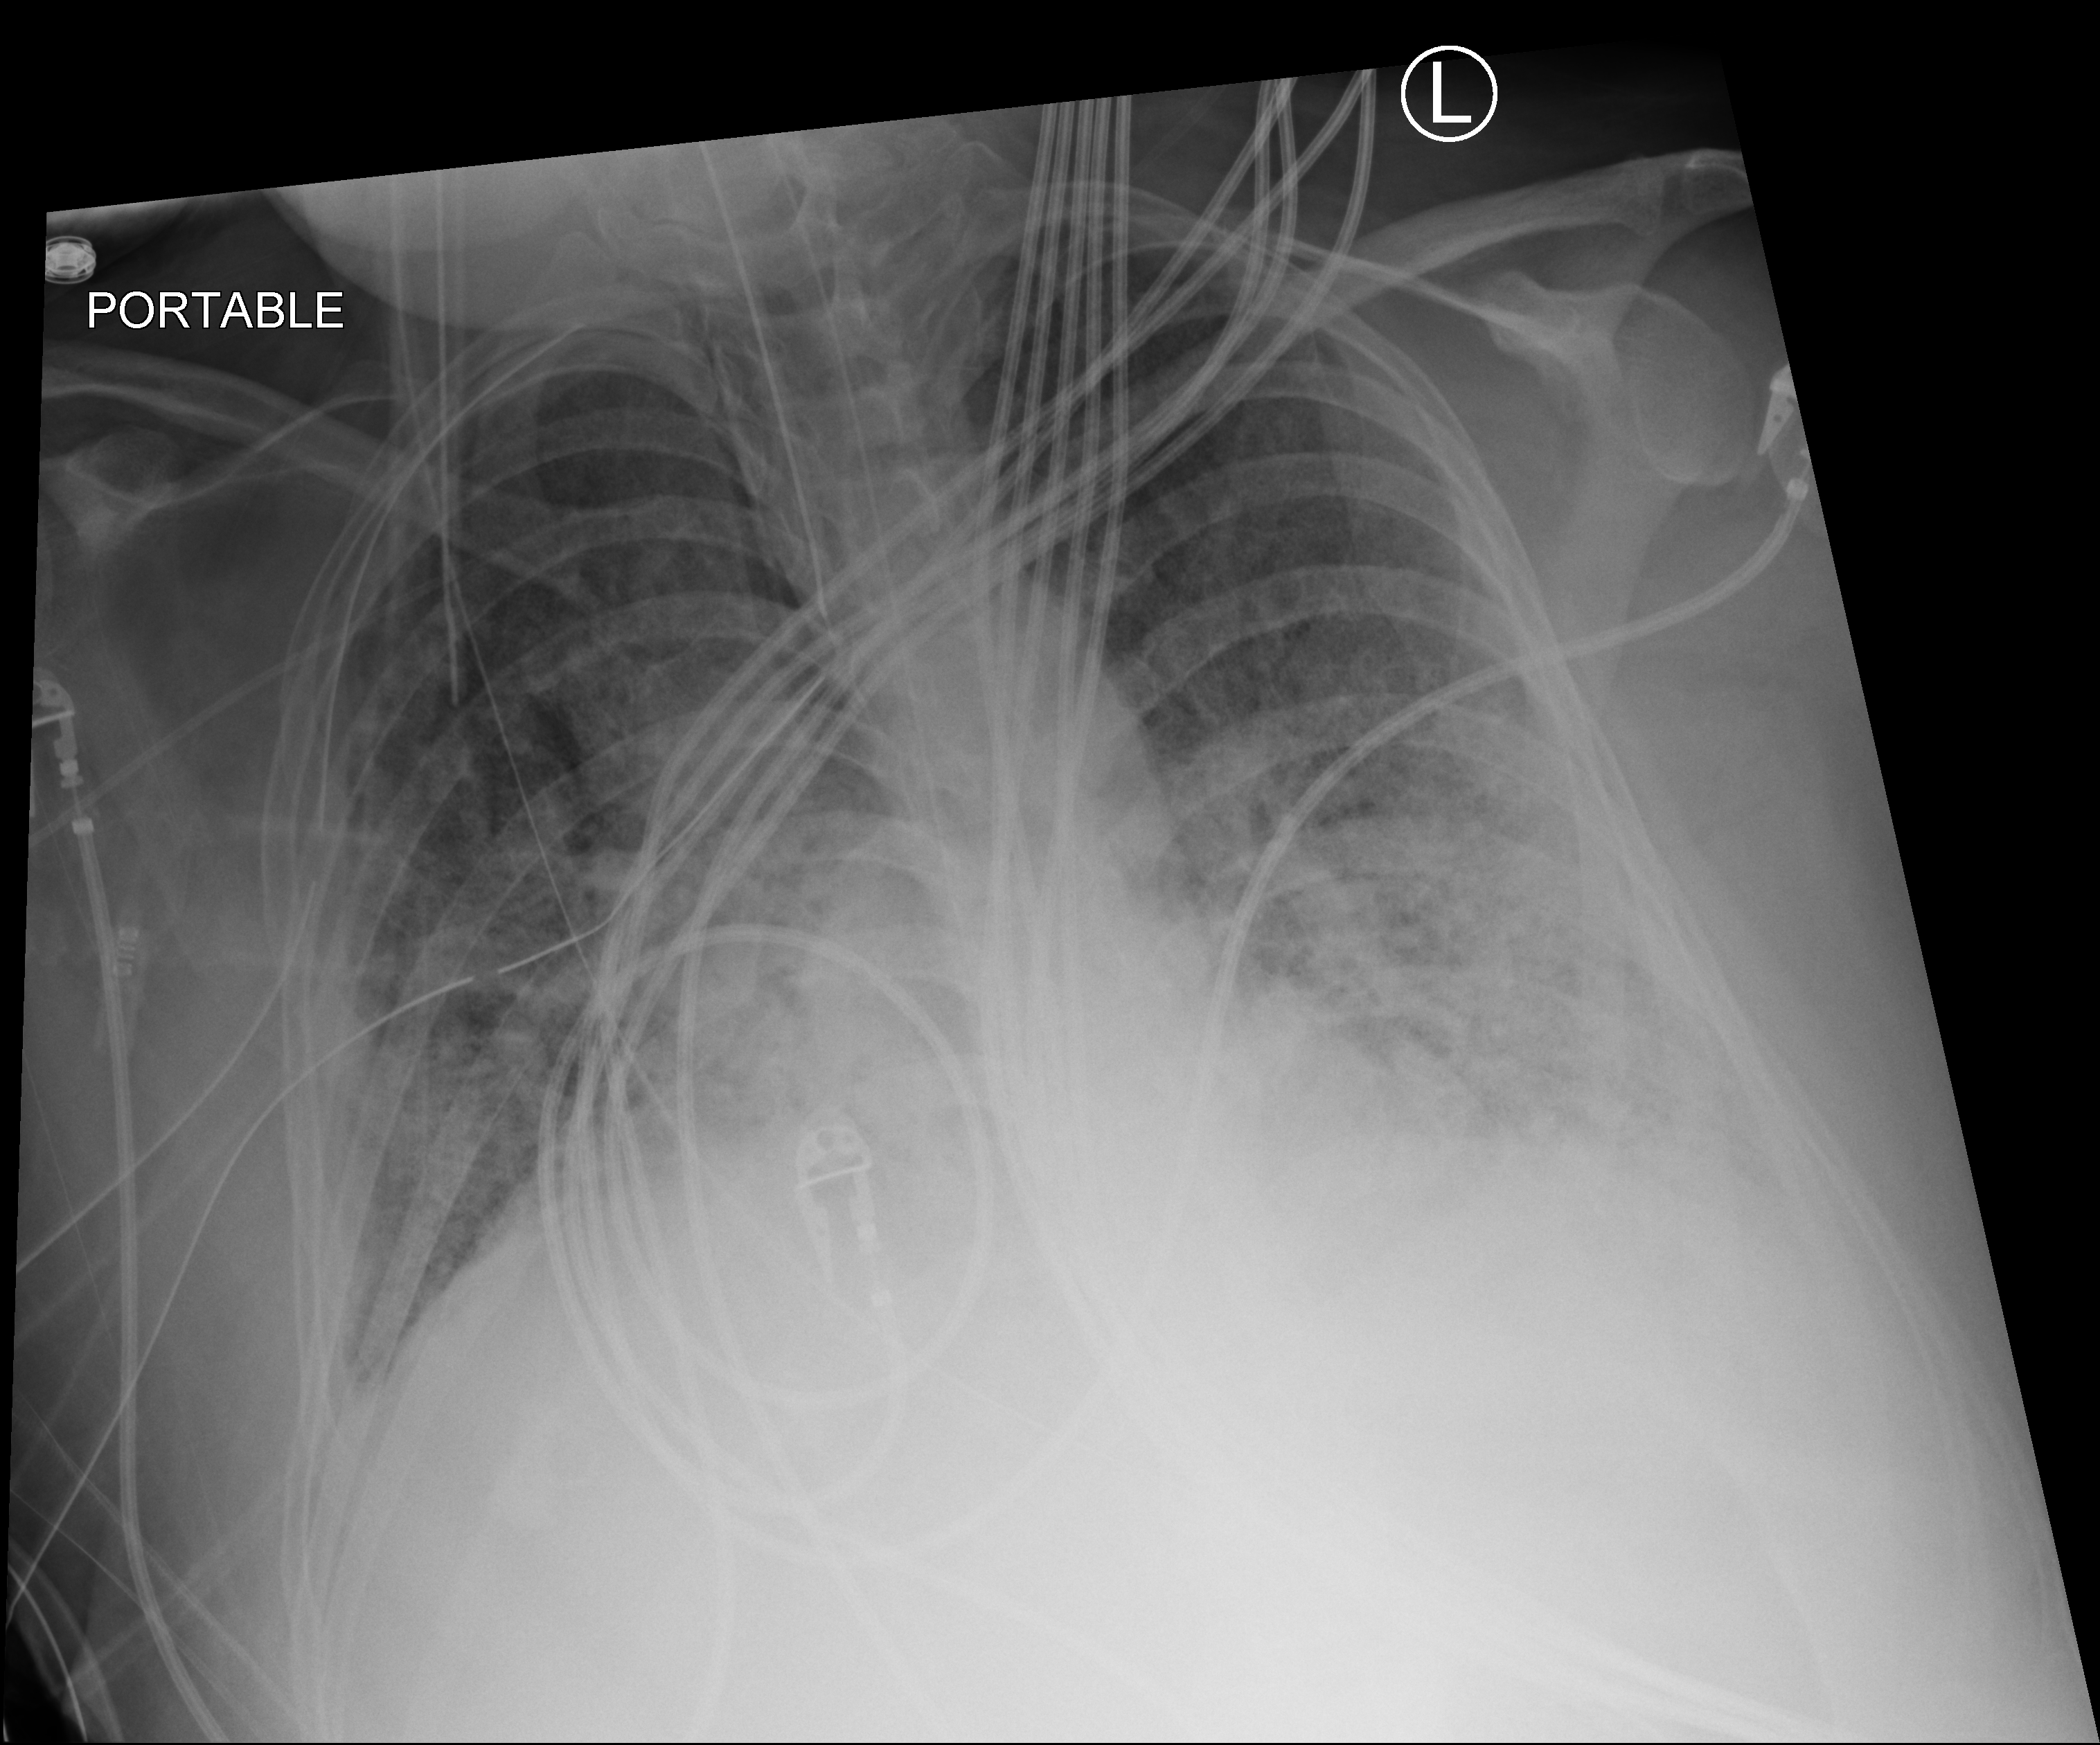
Chest X-ray (portable). Patient hospitalised with COVID-19, aged 18–59 years.
Admission-level facts for this patient (not findings on this image; timing relative to this image not recorded): mechanically ventilated during this hospital stay: yes.